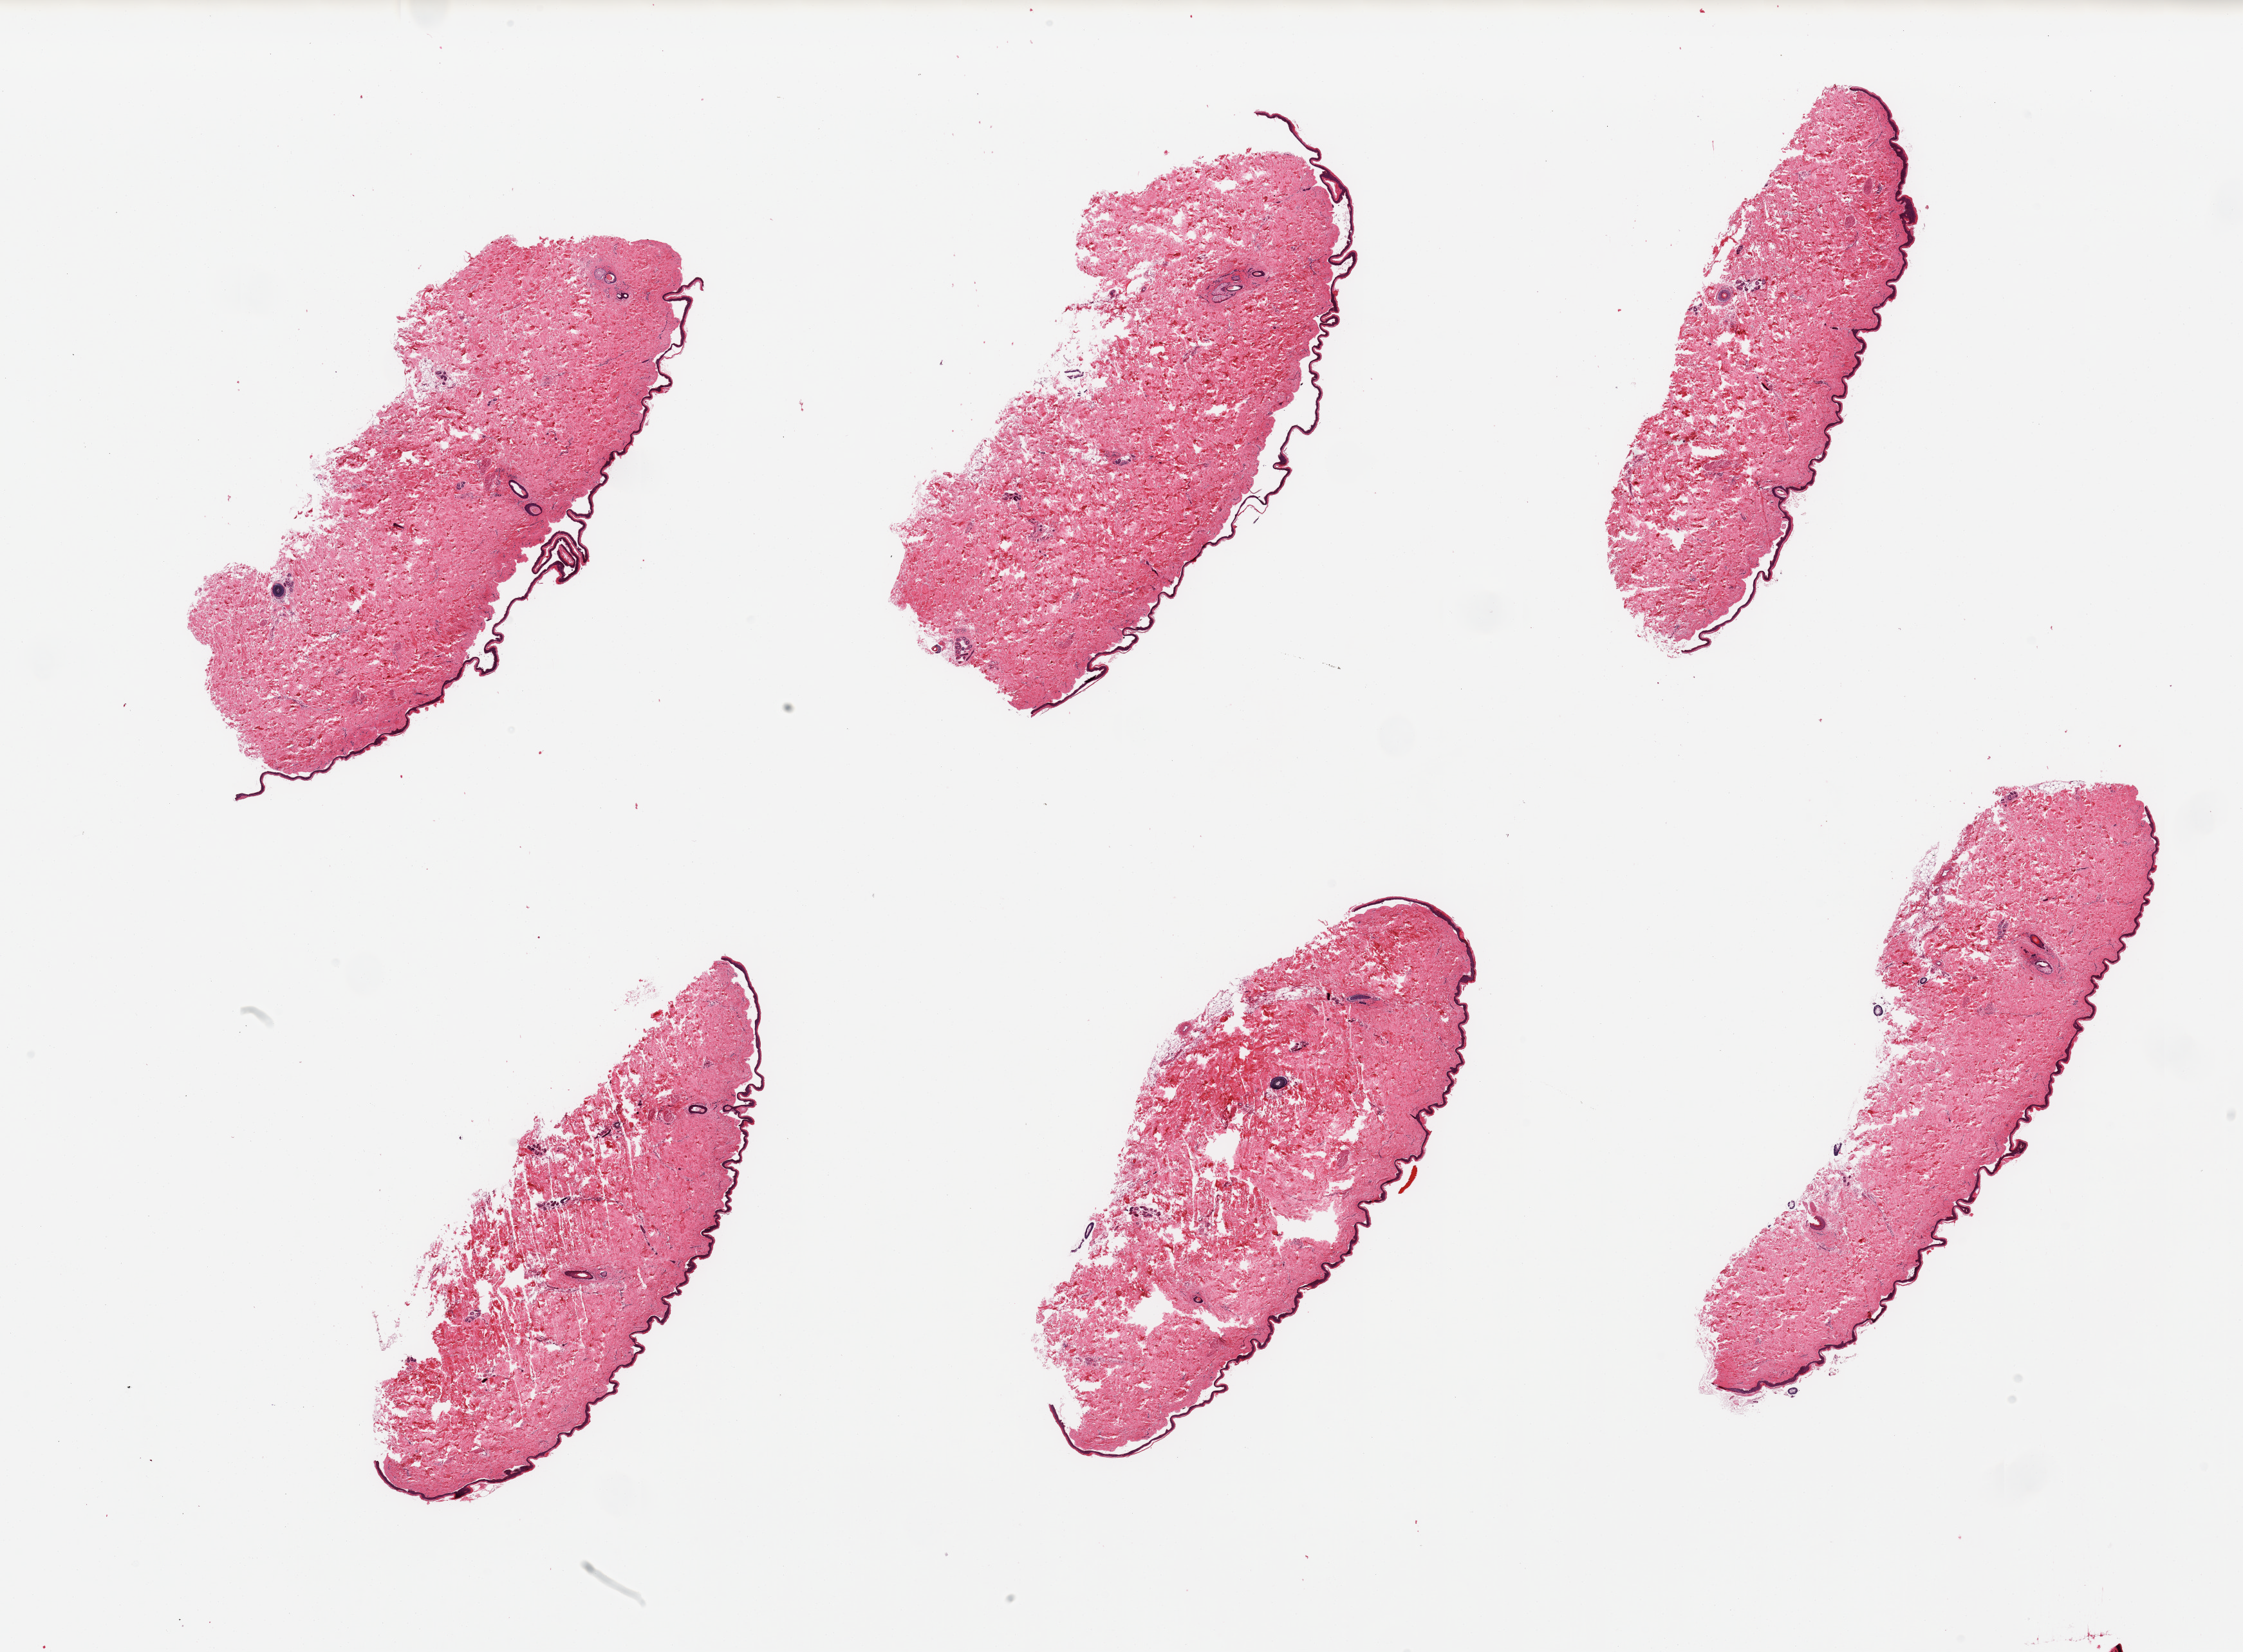
Whole-slide image, hematoxylin and eosin (H&E) stain, low-resolution overview of the scanned area, about 27.6 x 20.3 mm; PAXgene-fixed paraffin-embedded (PFPE) section; section of skin of suprapubic region (target tissue); donor tissue sample. Donor: female.
Pathologist's review note for this sample: 6 pieces; well trimmed, epidermis is largely detached.